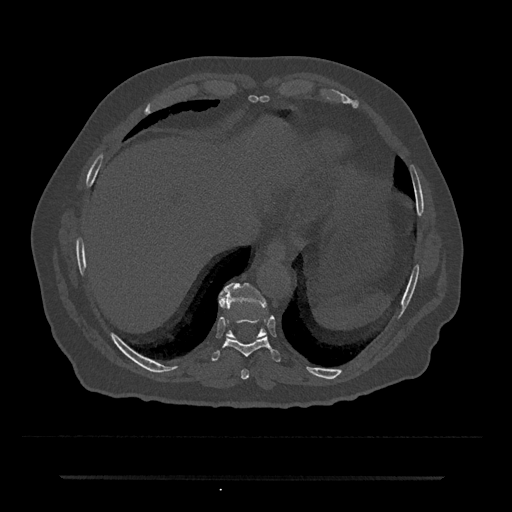
CT including the spine, one axial slice; position 267 of 797 along the scan axis; reconstruction kernel Br40s/3; 120 kVp; bone window (W 1800 / L 400 HU); 0.5 mm slice thickness; 512 × 512 image matrix, field of view 437 × 437 mm. Male patient, age 69 years. From the clinical record (not read from this slice): primary cancer: prostate.
Annotated regions visible in this slice (semi-automatic segmentation, software-assisted and operator-edited):
- T10 vertebra: bounding box [x1, y1, x2, y2] px = [219, 282, 267, 339]
- T8 vertebra: [241, 369, 249, 380]
- T9 vertebra: [211, 291, 281, 362]